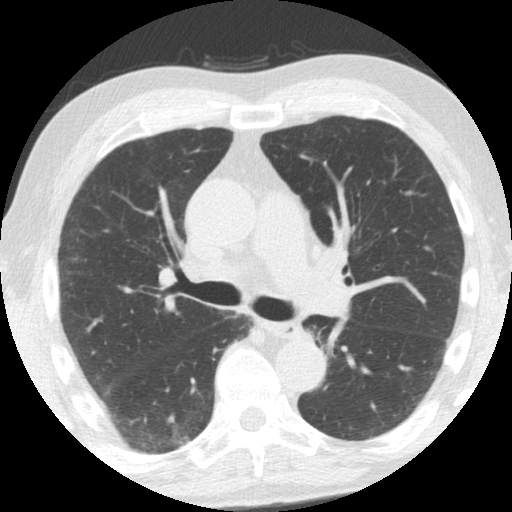
Chest CT (low-dose screening protocol), one axial image, third annual screen, lung window (W 1500 / L -600 HU), 2.5 mm slice thickness, 120 kVp, slice 50 of 108 in the series, 512 × 512 image matrix, field of view 308 × 308 mm. Male, age 61 years at enrolment. Former smoker at enrolment.
Lesion marked by an expert reader, box from (x=292, y=316) to (x=345, y=363) px. No non-calcified nodule or mass ≥4 mm was recorded by the screening reader at this exam. Official screen result: negative screen, minor abnormalities not suspicious for lung cancer. Lung cancer was diagnosed 363 days after this screen: squamous cell carcinoma, NOS, left upper lobe, left lower lobe, well differentiated (G1), stage IIB (AJCC 6th edition), 100 mm at pathology.